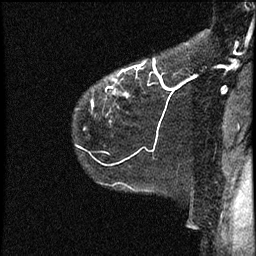
Breast MRI (dynamic contrast-enhanced), one sagittal slice. Slice 39 of 44 in the series (ordered by position). Dynamic contrast-enhanced study with each time point stored as its own series, time point 2 of 4 at this slice position (early post-contrast, ordered by acquisition time). 1.5 T. TE 4.2 ms, TR 17.7 ms. 2 mm slice thickness. 256 × 256 image matrix. Female patient, age 52 years. From the clinical record (not read from this slice): setting: breast cancer imaged before/during neoadjuvant chemotherapy; receptor status: HR-positive, HER2-negative.
Annotated regions visible in this slice (semi-automatic segmentation, software-assisted and operator-edited):
- analysis volume of interest (the breast-tissue region the enhancement analysis was run in; not a lesion): bounding box [x1, y1, x2, y2] px = [72, 54, 163, 147]
- tumour enhancement mask (voxels above the 100 % enhancement threshold inside the analysis volume of interest): [91, 59, 163, 106]